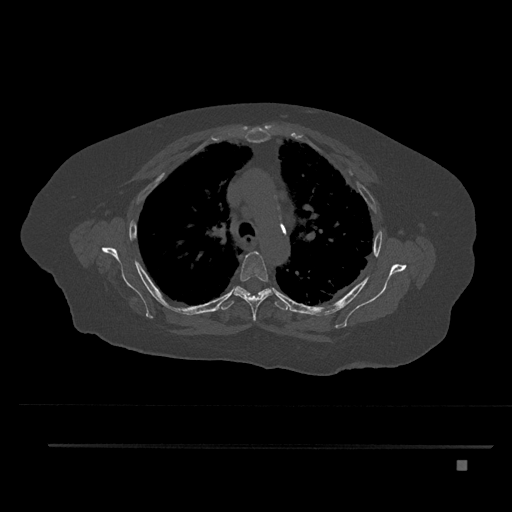
CT including the spine, one axial slice. Slice 593 of 797 in the series (ordered by position). Reconstruction kernel Br40s/3. Bone window (W 1800 / L 400 HU). 512 × 512 image matrix. Patient: female, 76 years. Case-level facts recorded for this patient, not image findings: primary cancer: lung; vertebrae with lytic lesions (as recorded): T11, L3.
Structures marked on this image (semi-automatically segmented with operator editing):
- T4 vertebra: box from (x=234, y=251) to (x=272, y=321) px
- T5 vertebra: (x=220, y=286)–(x=289, y=311)